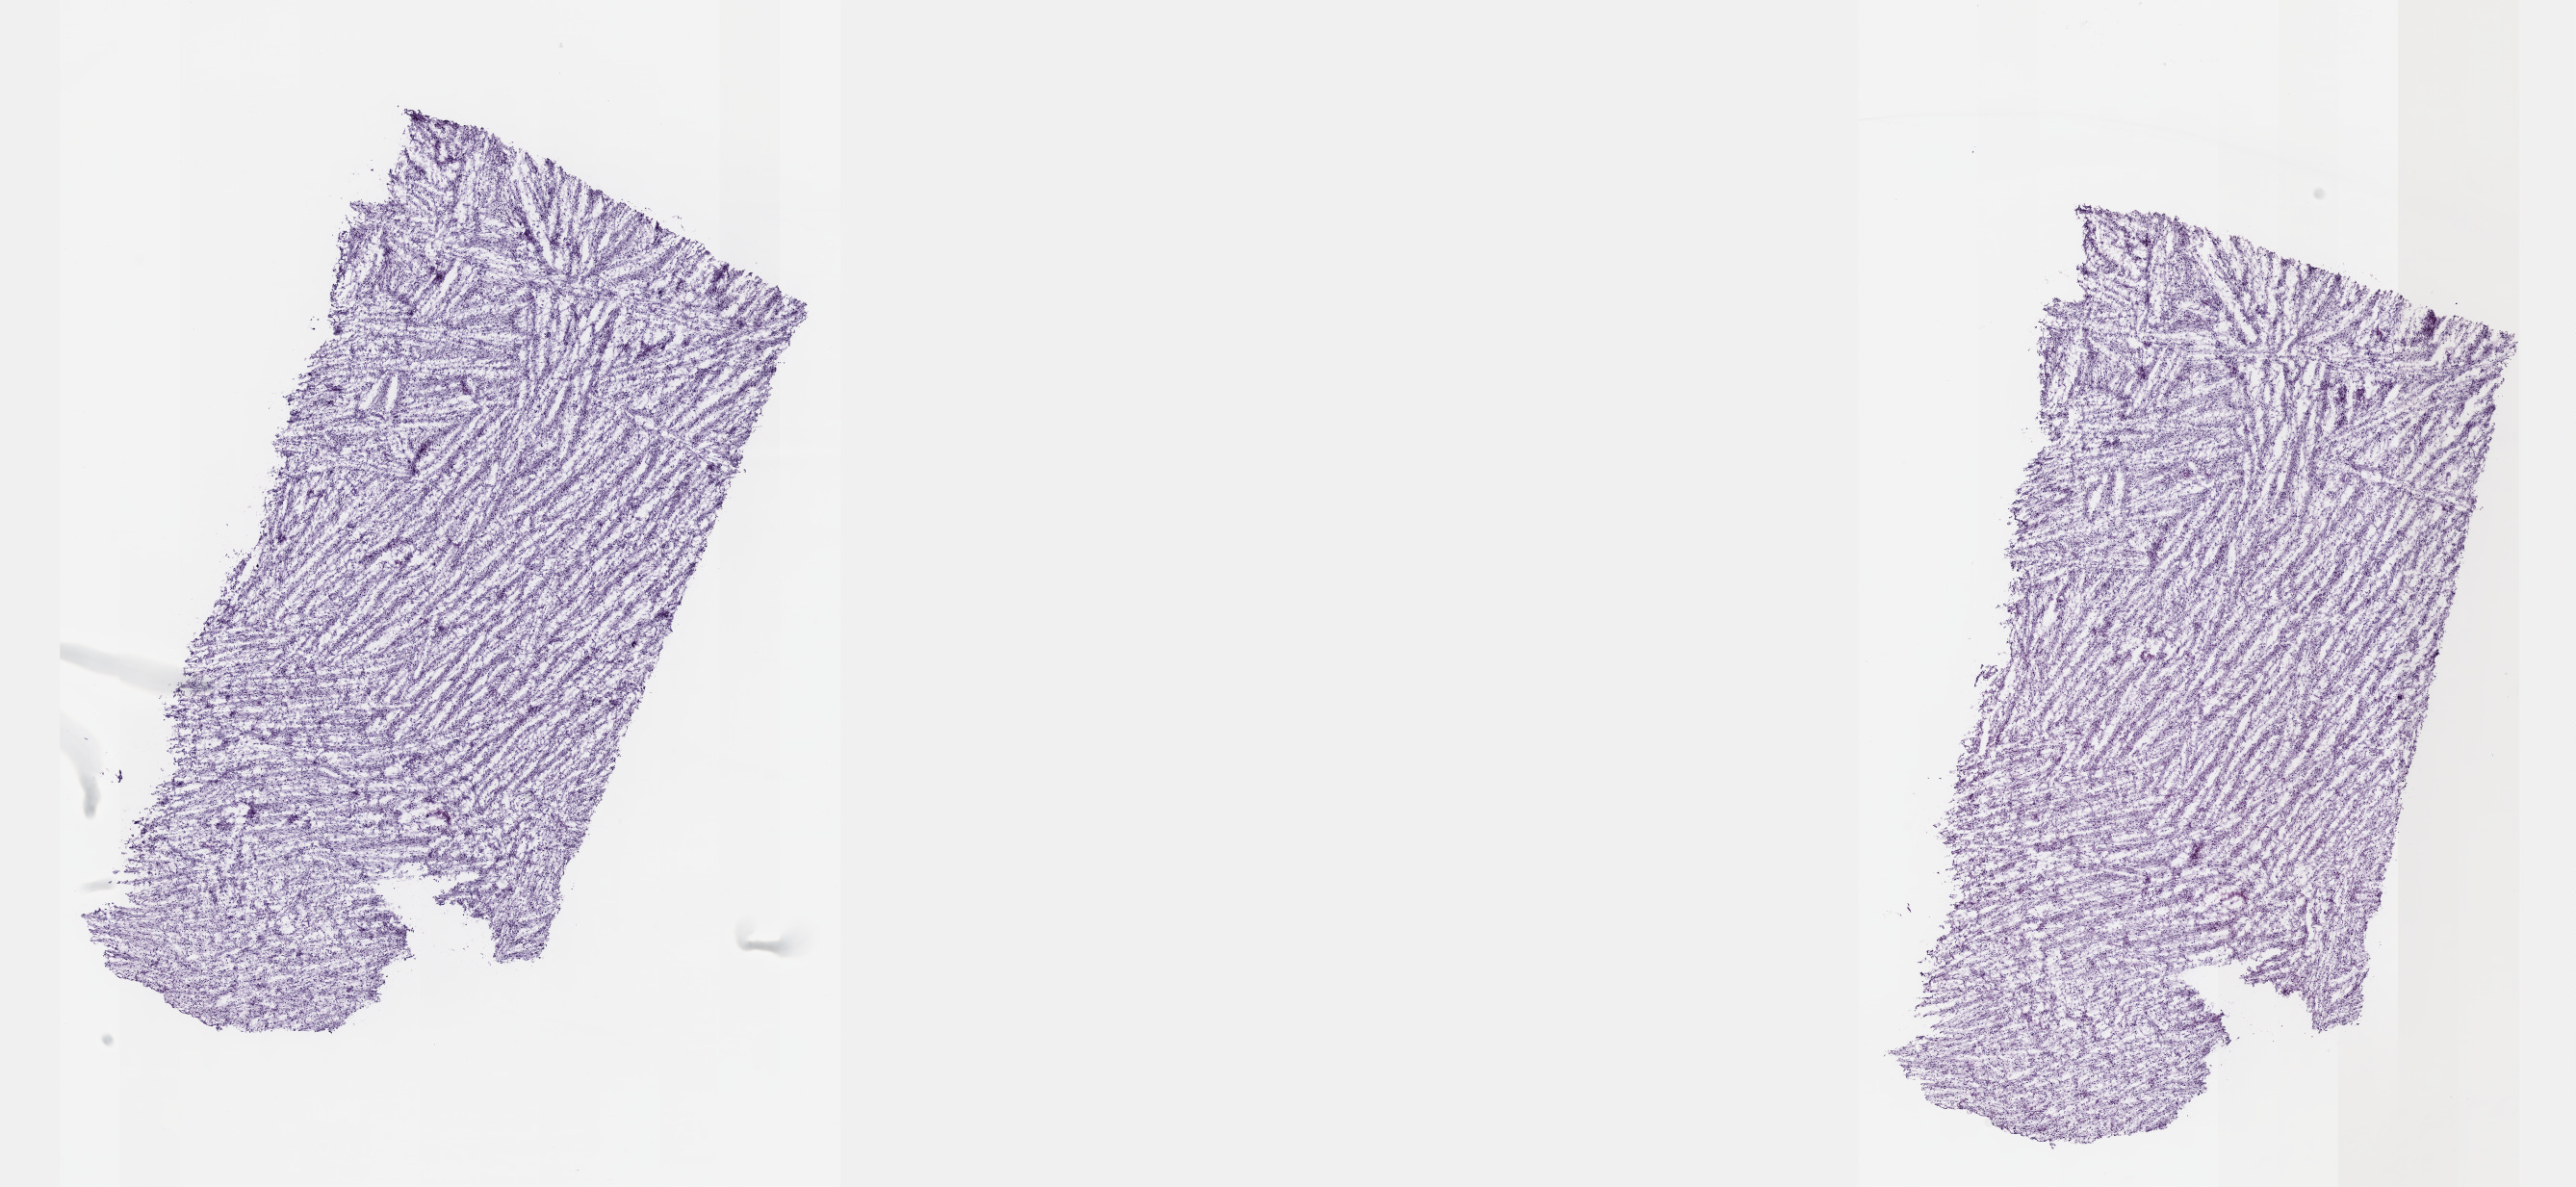
Digitized H&E-stained tissue section (whole slide) — shown as a low-resolution overview of the whole scanned area (about 21.6 x 10.0 mm, slide scanned at 40x), frozen section, primary tumour sample from the colon. Male, age 65 years at initial diagnosis. Pathologist review of this section (percent, as recorded): tumour cells 100%, tumour nuclei 95%, normal cells 0%, stromal cells 0%, necrosis 0%. Infiltration values recorded for this section: lymphocyte infiltration 0%, monocyte infiltration 0%, neutrophil infiltration 0%.
- pathologic diagnosis: Dedifferentiated liposarcoma (descending colon)